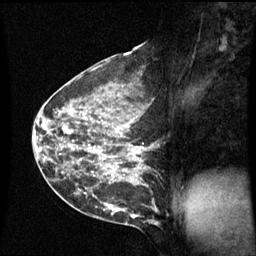
Breast MRI (dynamic contrast-enhanced), one sagittal slice; dynamic contrast-enhanced series, image 2 of 3 at this slice position (ordered by acquisition); 1.5 T; TE 4.2 ms, TR 8.9 ms; 2.4 mm slice thickness; 256 × 256 image matrix, field of view 210 × 210 mm. Female patient, age 42 years. Case-level facts recorded for this patient, not image findings: setting: breast cancer imaged before/during neoadjuvant chemotherapy; receptor status: HER2-positive.
Outlined on this slice (semi-automatic segmentation, software-assisted and operator-edited):
- analysis volume of interest (the breast-tissue region the enhancement analysis was run in; not a lesion): box from (x=62, y=93) to (x=153, y=210) px
- tumour enhancement mask (voxels above the 70 % enhancement threshold inside the analysis volume of interest): (x=65, y=126)–(x=136, y=158)